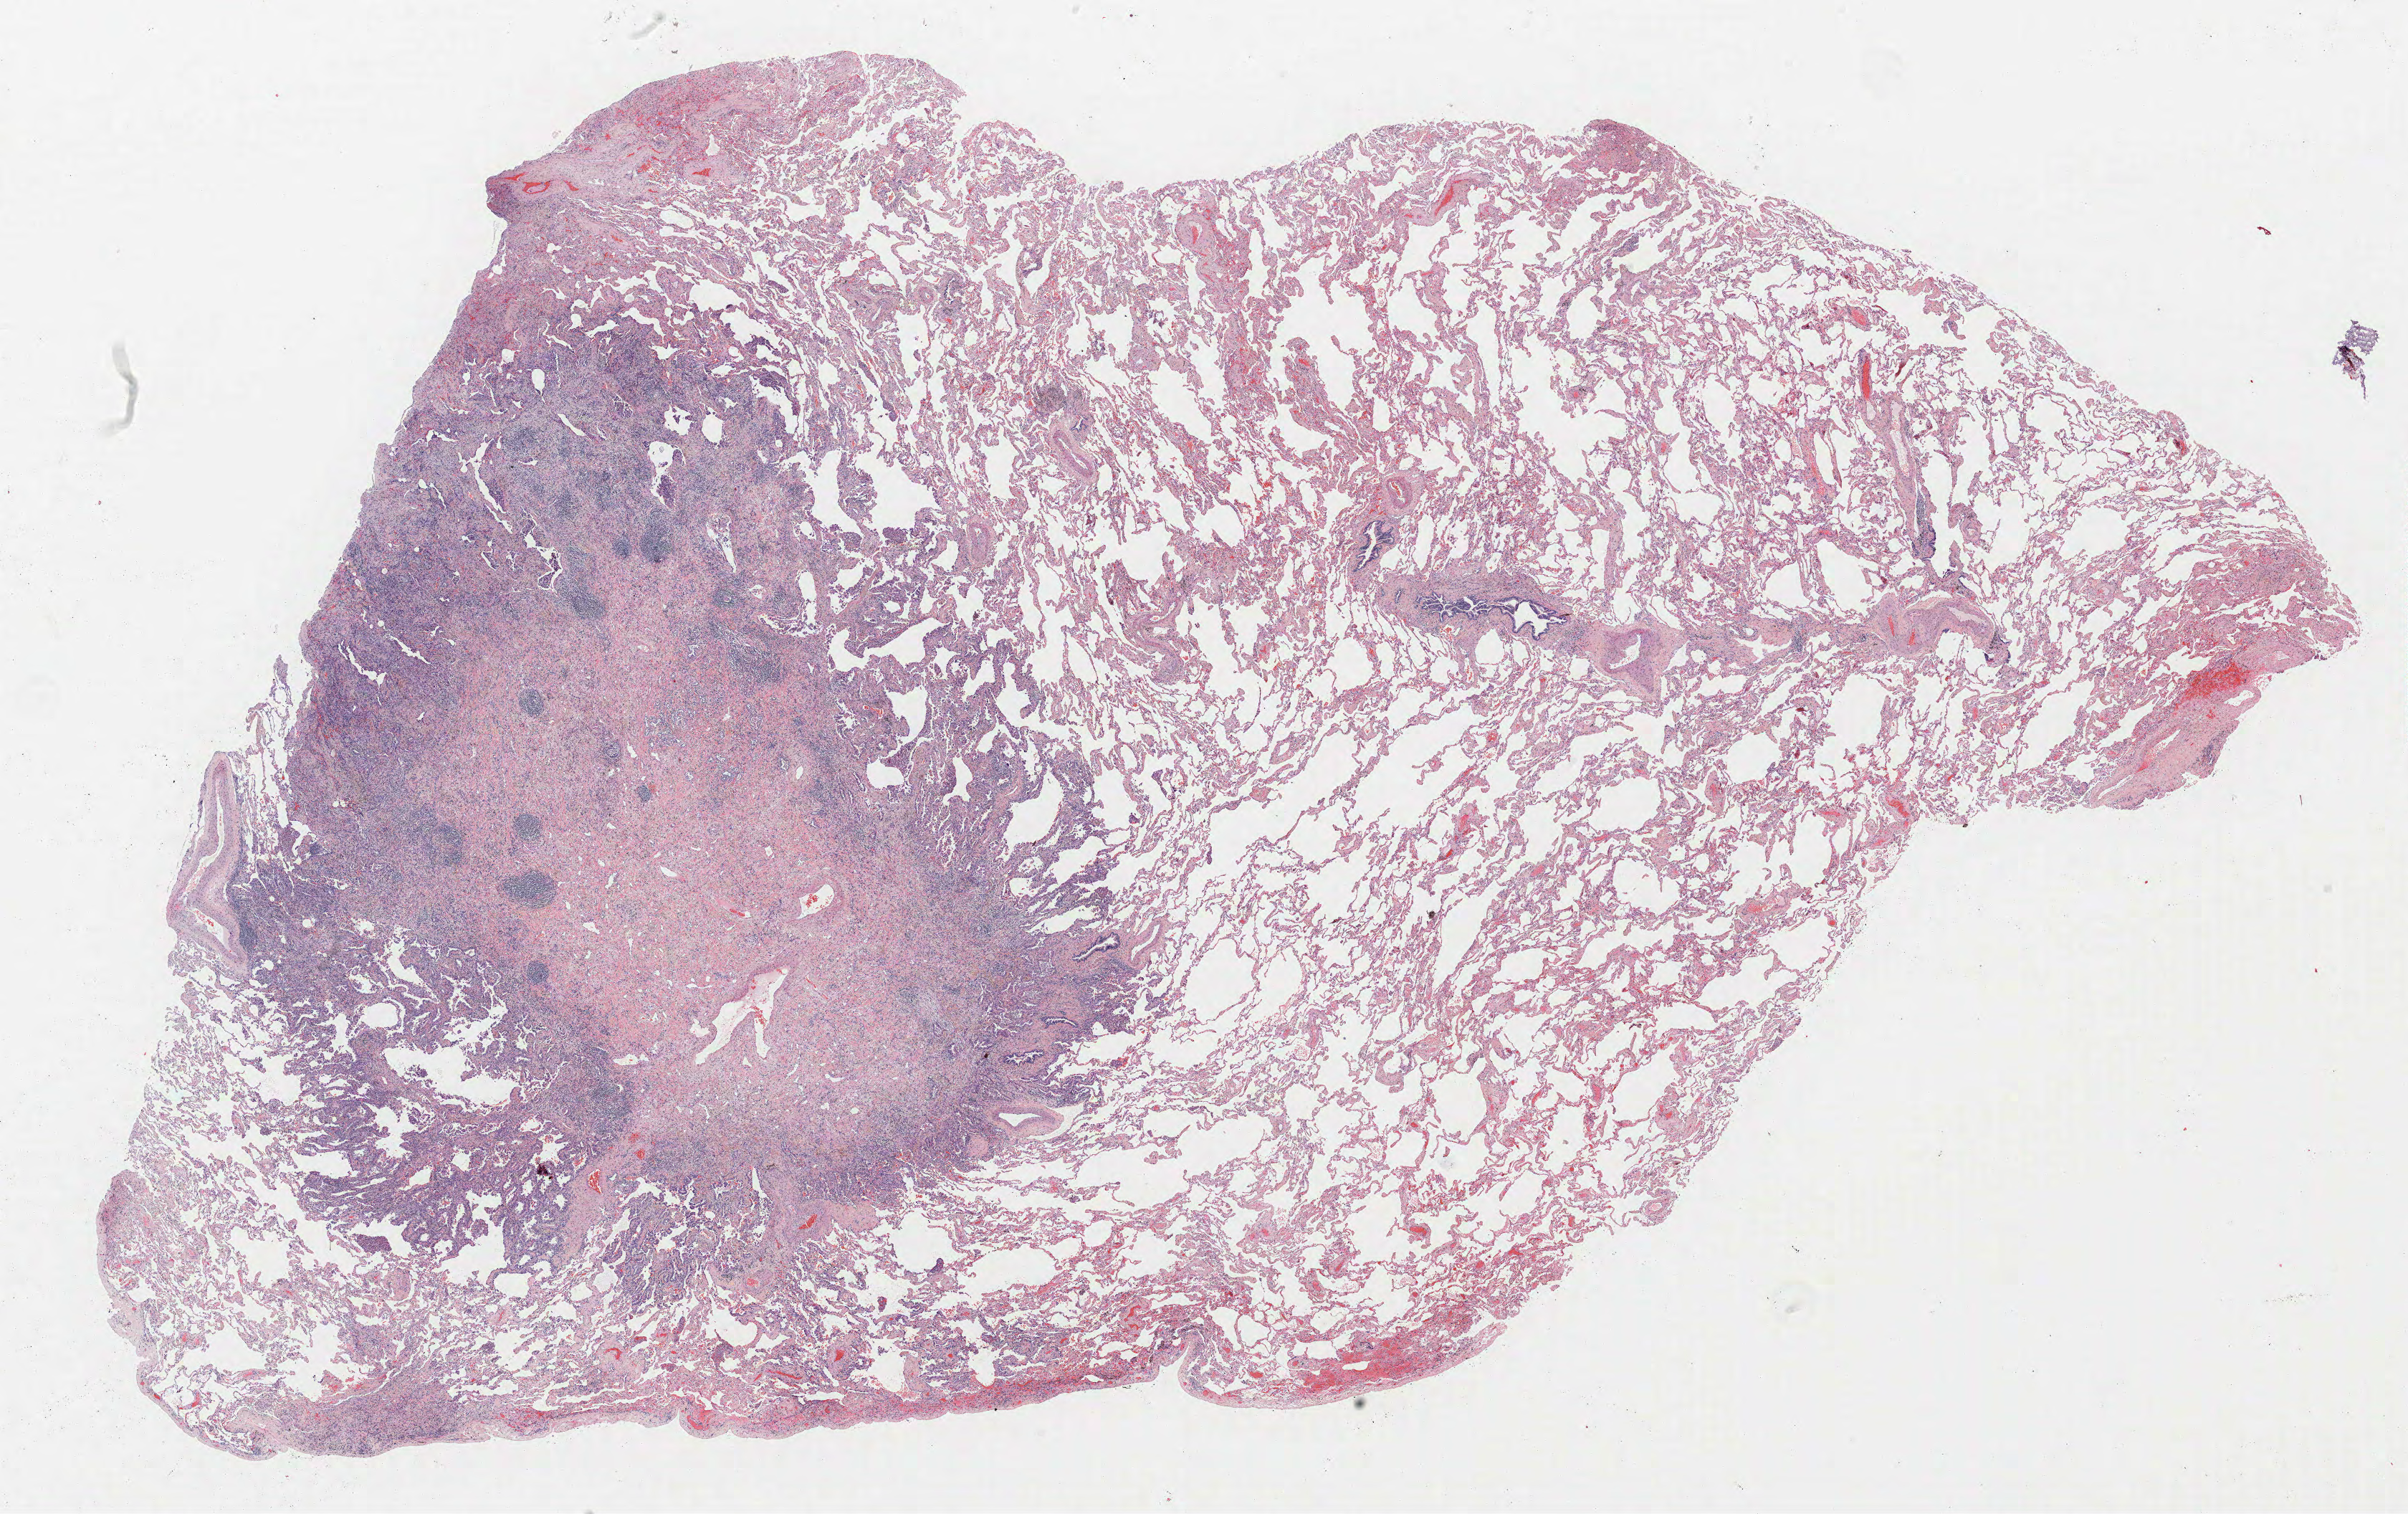
Whole-slide histology image, Hematoxylin and eosin (H&E) stained, shown as a low-resolution overview of the whole scanned area (about 26.9 x 16.9 mm, from a 40x scan), formalin-fixed paraffin-embedded (FFPE) section, lung tissue. Female patient, aged 64 at enrolment. Former smoker at enrolment.
Participant's lung-cancer diagnosis: Bronchiolo-alveolar adenocarcinoma, NOS.